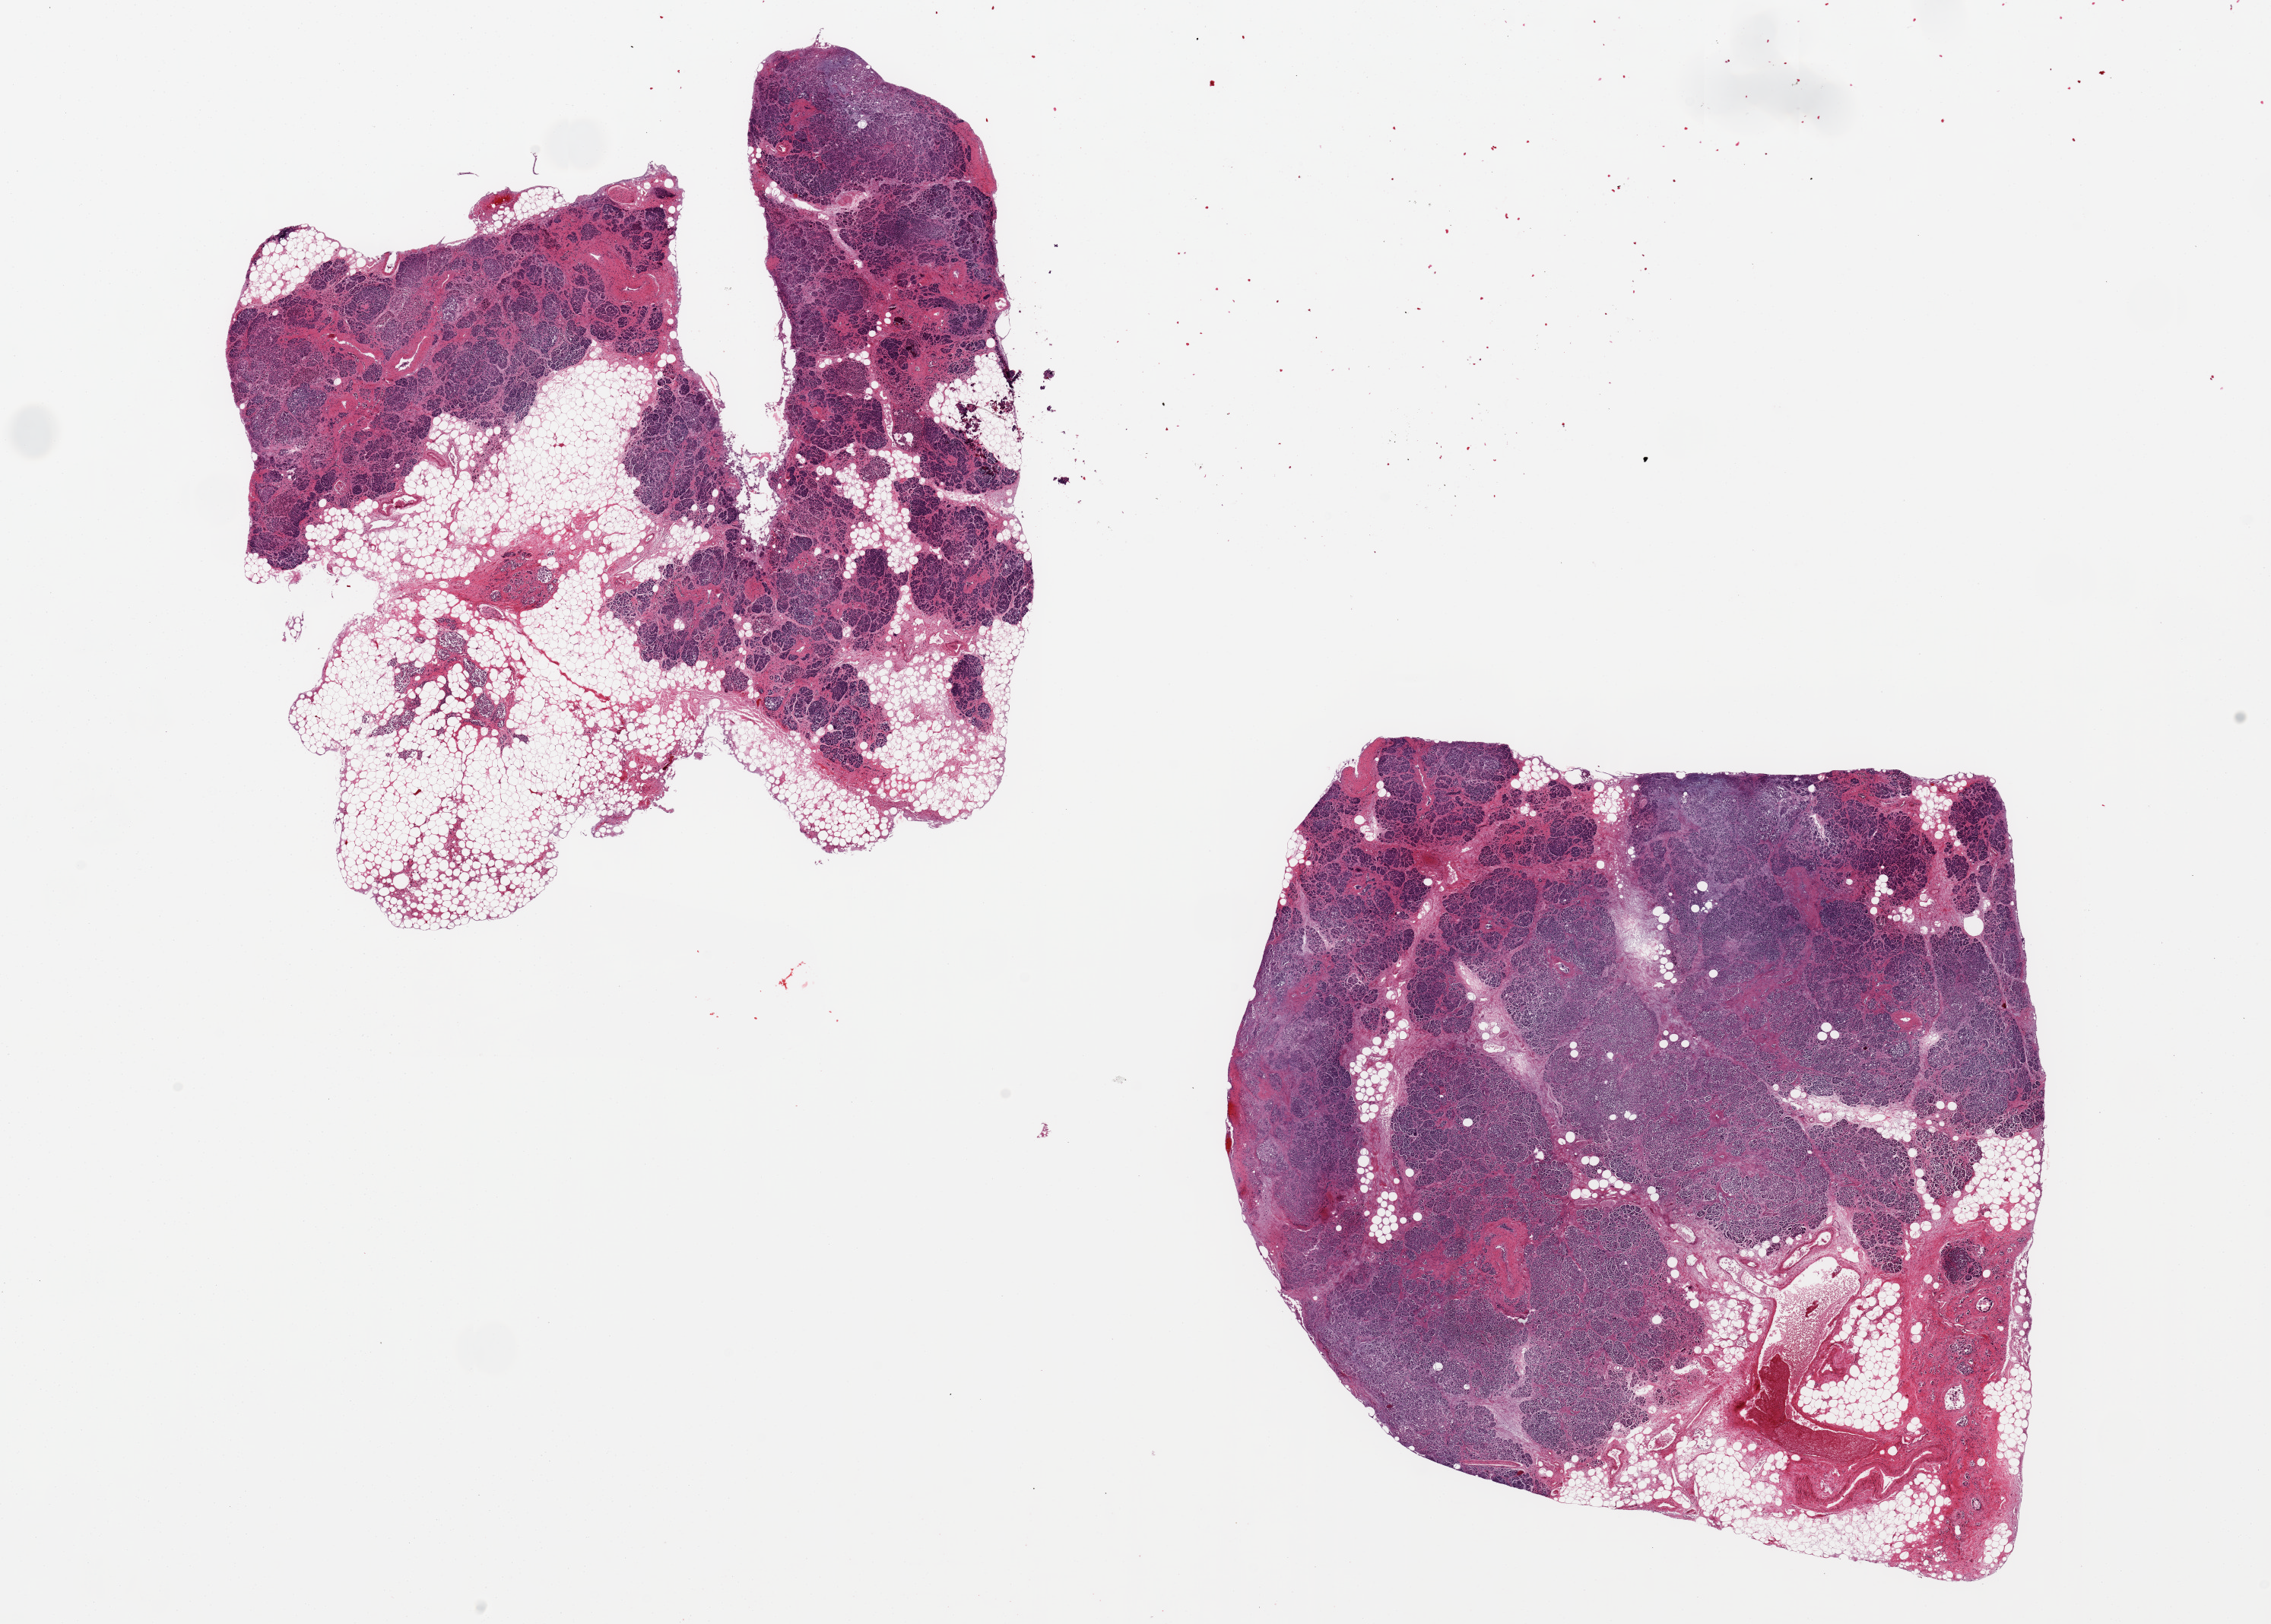
Whole-slide image, hematoxylin and eosin (H&E) stain, shown as a low-resolution overview of the whole scanned area (about 23.6 x 16.9 mm). PAXgene-fixed paraffin-embedded (PFPE) section. Sampled site (target tissue): pancreas. Tissue donor sample. Male donor.
Pathologist's review note for this sample: 2 pieces, each 8x8 mm; 50% adipose in 1, 30% in the other.